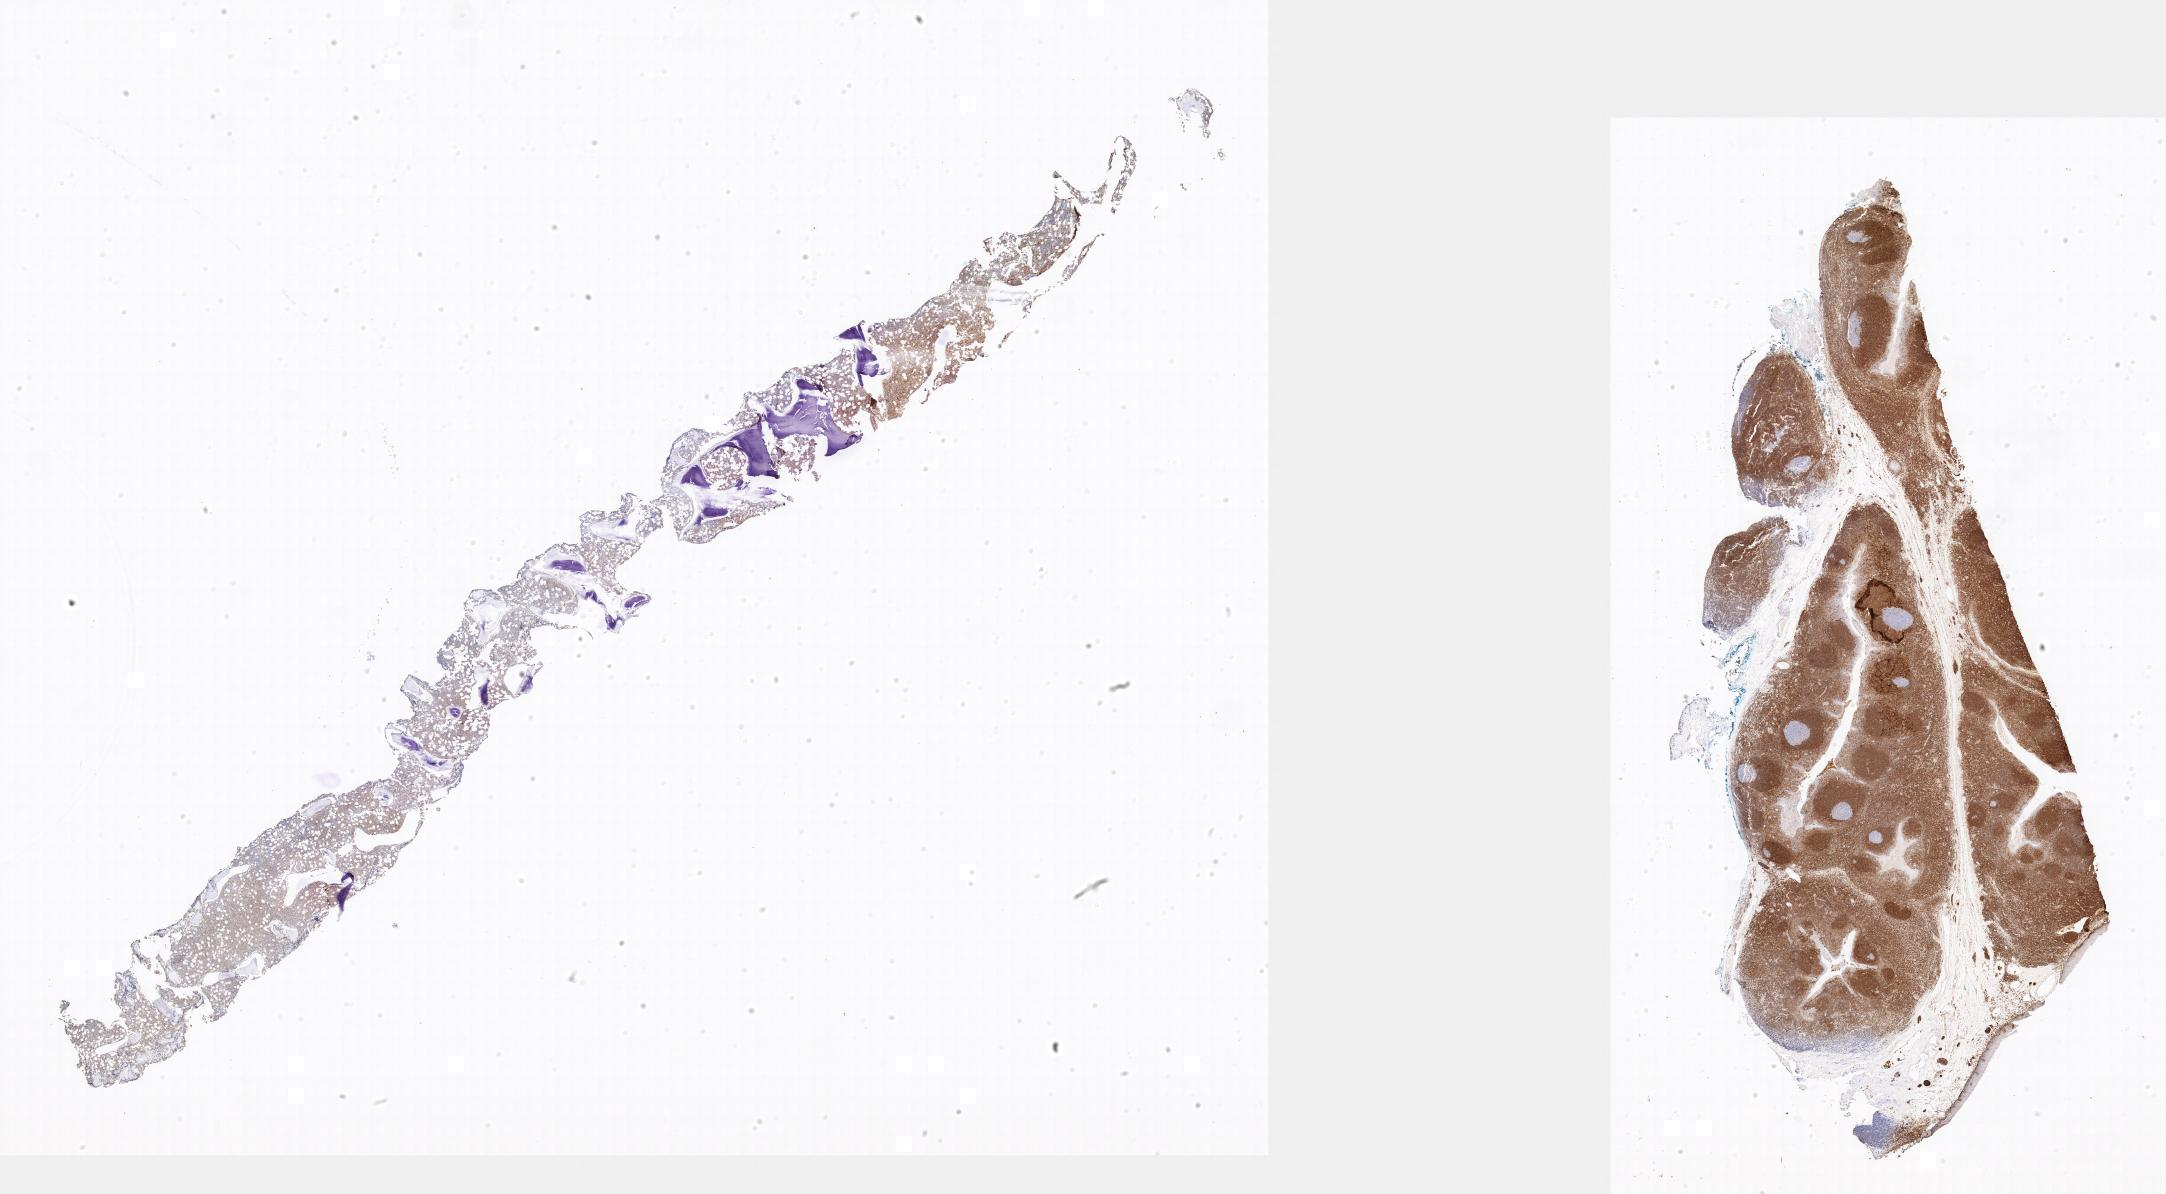
Immunohistochemistry (IHC) whole-slide image stained for BCL2 — low-resolution overview of the scanned area, specimen: tumor tissue, site: bone marrow. Patient male; aged 20.
Histologic diagnosis: Diffuse large B-cell lymphoma, NOS.